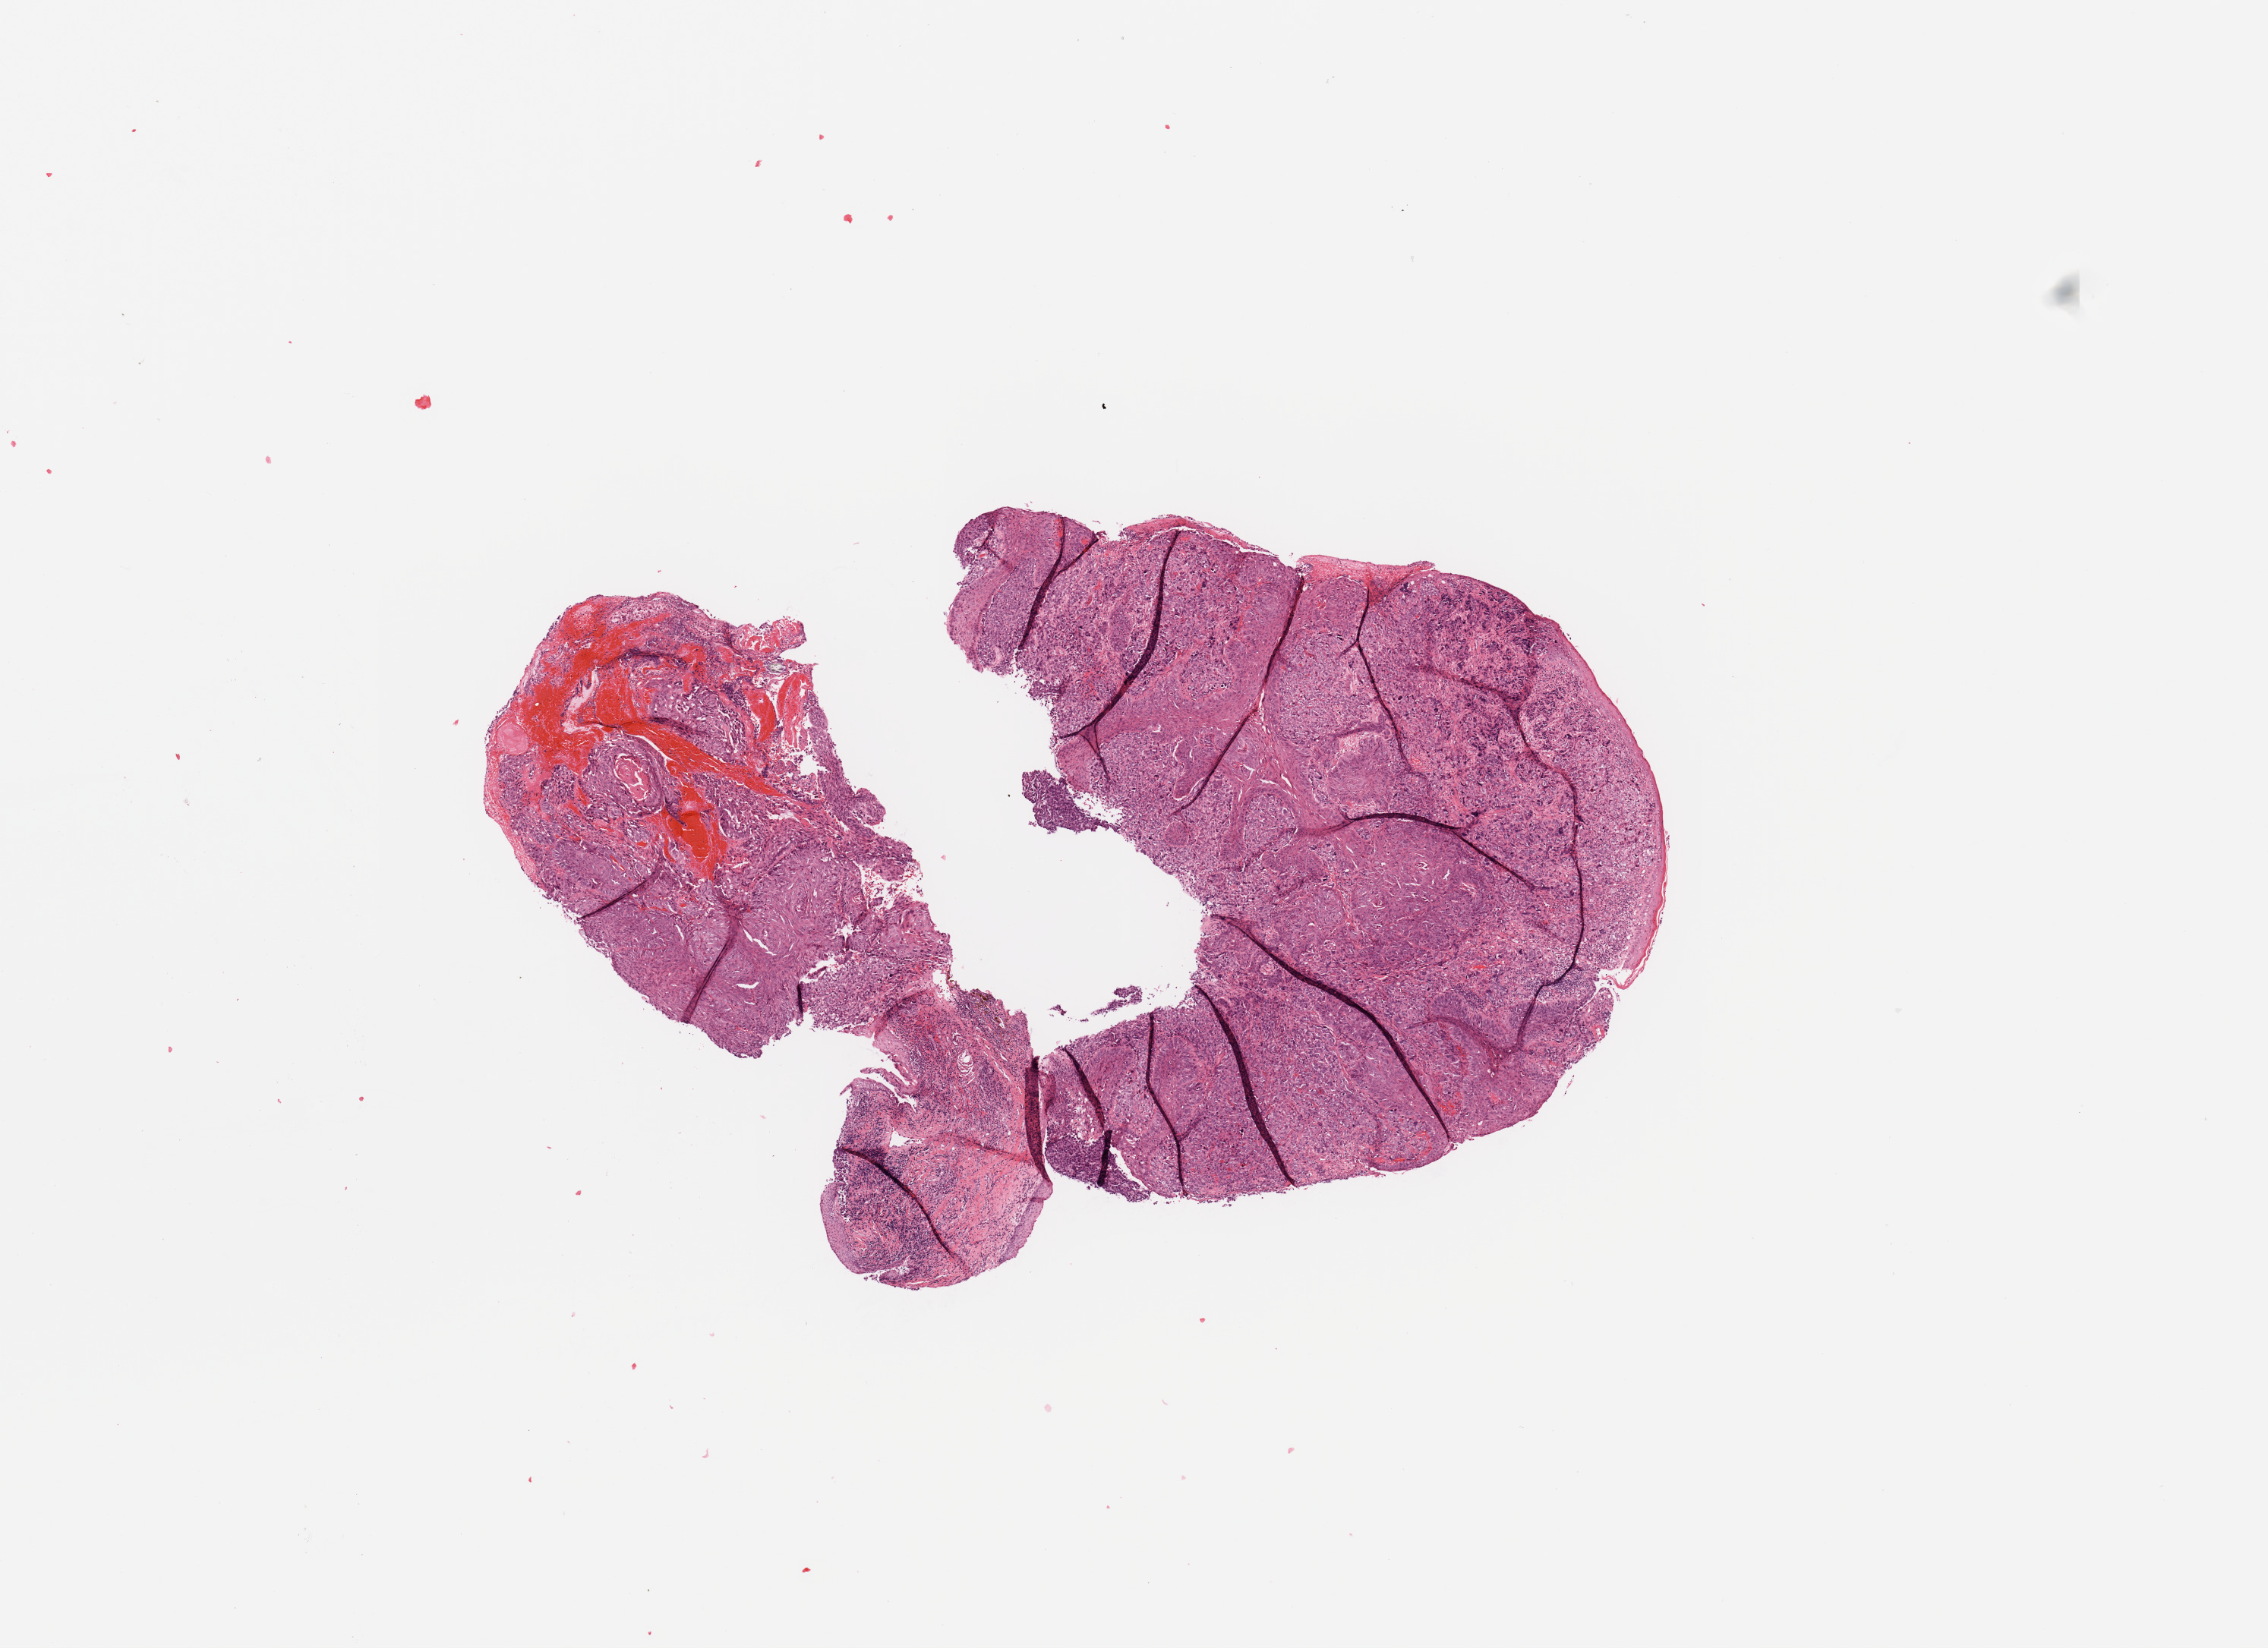
Digitized Hematoxylin and eosin (H&E) stained tissue section (whole slide), shown as a low-resolution overview of the whole scanned area (about 11.8 x 8.6 mm, from a 20x scan); tumour tissue sample, sampled site: larynx. Female, 63 y/o. Histologic grade: G3 (poorly differentiated). Slide review estimates, as recorded: tumour nuclei 85%, necrosis 5%.
Histologic diagnosis: Squamous cell carcinoma, NOS (larynx, NOS). AJCC pathologic stage: III.